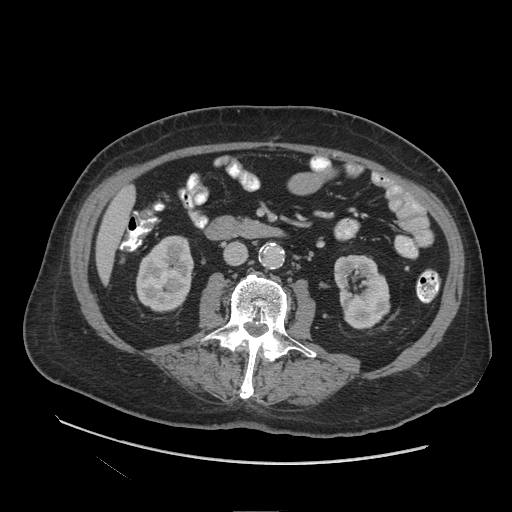
Contrast-enhanced abdominal CT (liver protocol), one axial slice. Slice 25 of 109 in the series (ordered by position). Reconstruction kernel STANDARD. 140 kVp. Soft-tissue window (W 400 / L 40 HU). 2.5 mm slice thickness. 512 × 512 image matrix, field of view 420 × 420 mm. From the clinical record (not read from this slice): diagnosis: hepatocellular carcinoma (patient treated with transarterial chemoembolisation; whether this scan precedes or follows treatment is not stated here); TNM stage (as recorded): Stage-I; Child-Pugh class: A; tumour nodularity: uninodular.
Annotated regions visible in this slice (semi-automatic segmentation, software-assisted and operator-edited):
- liver parenchyma outside the tumour (the mass and vessels are separate outlines, so this box may not span the whole liver): box from (x=96, y=186) to (x=134, y=282) px